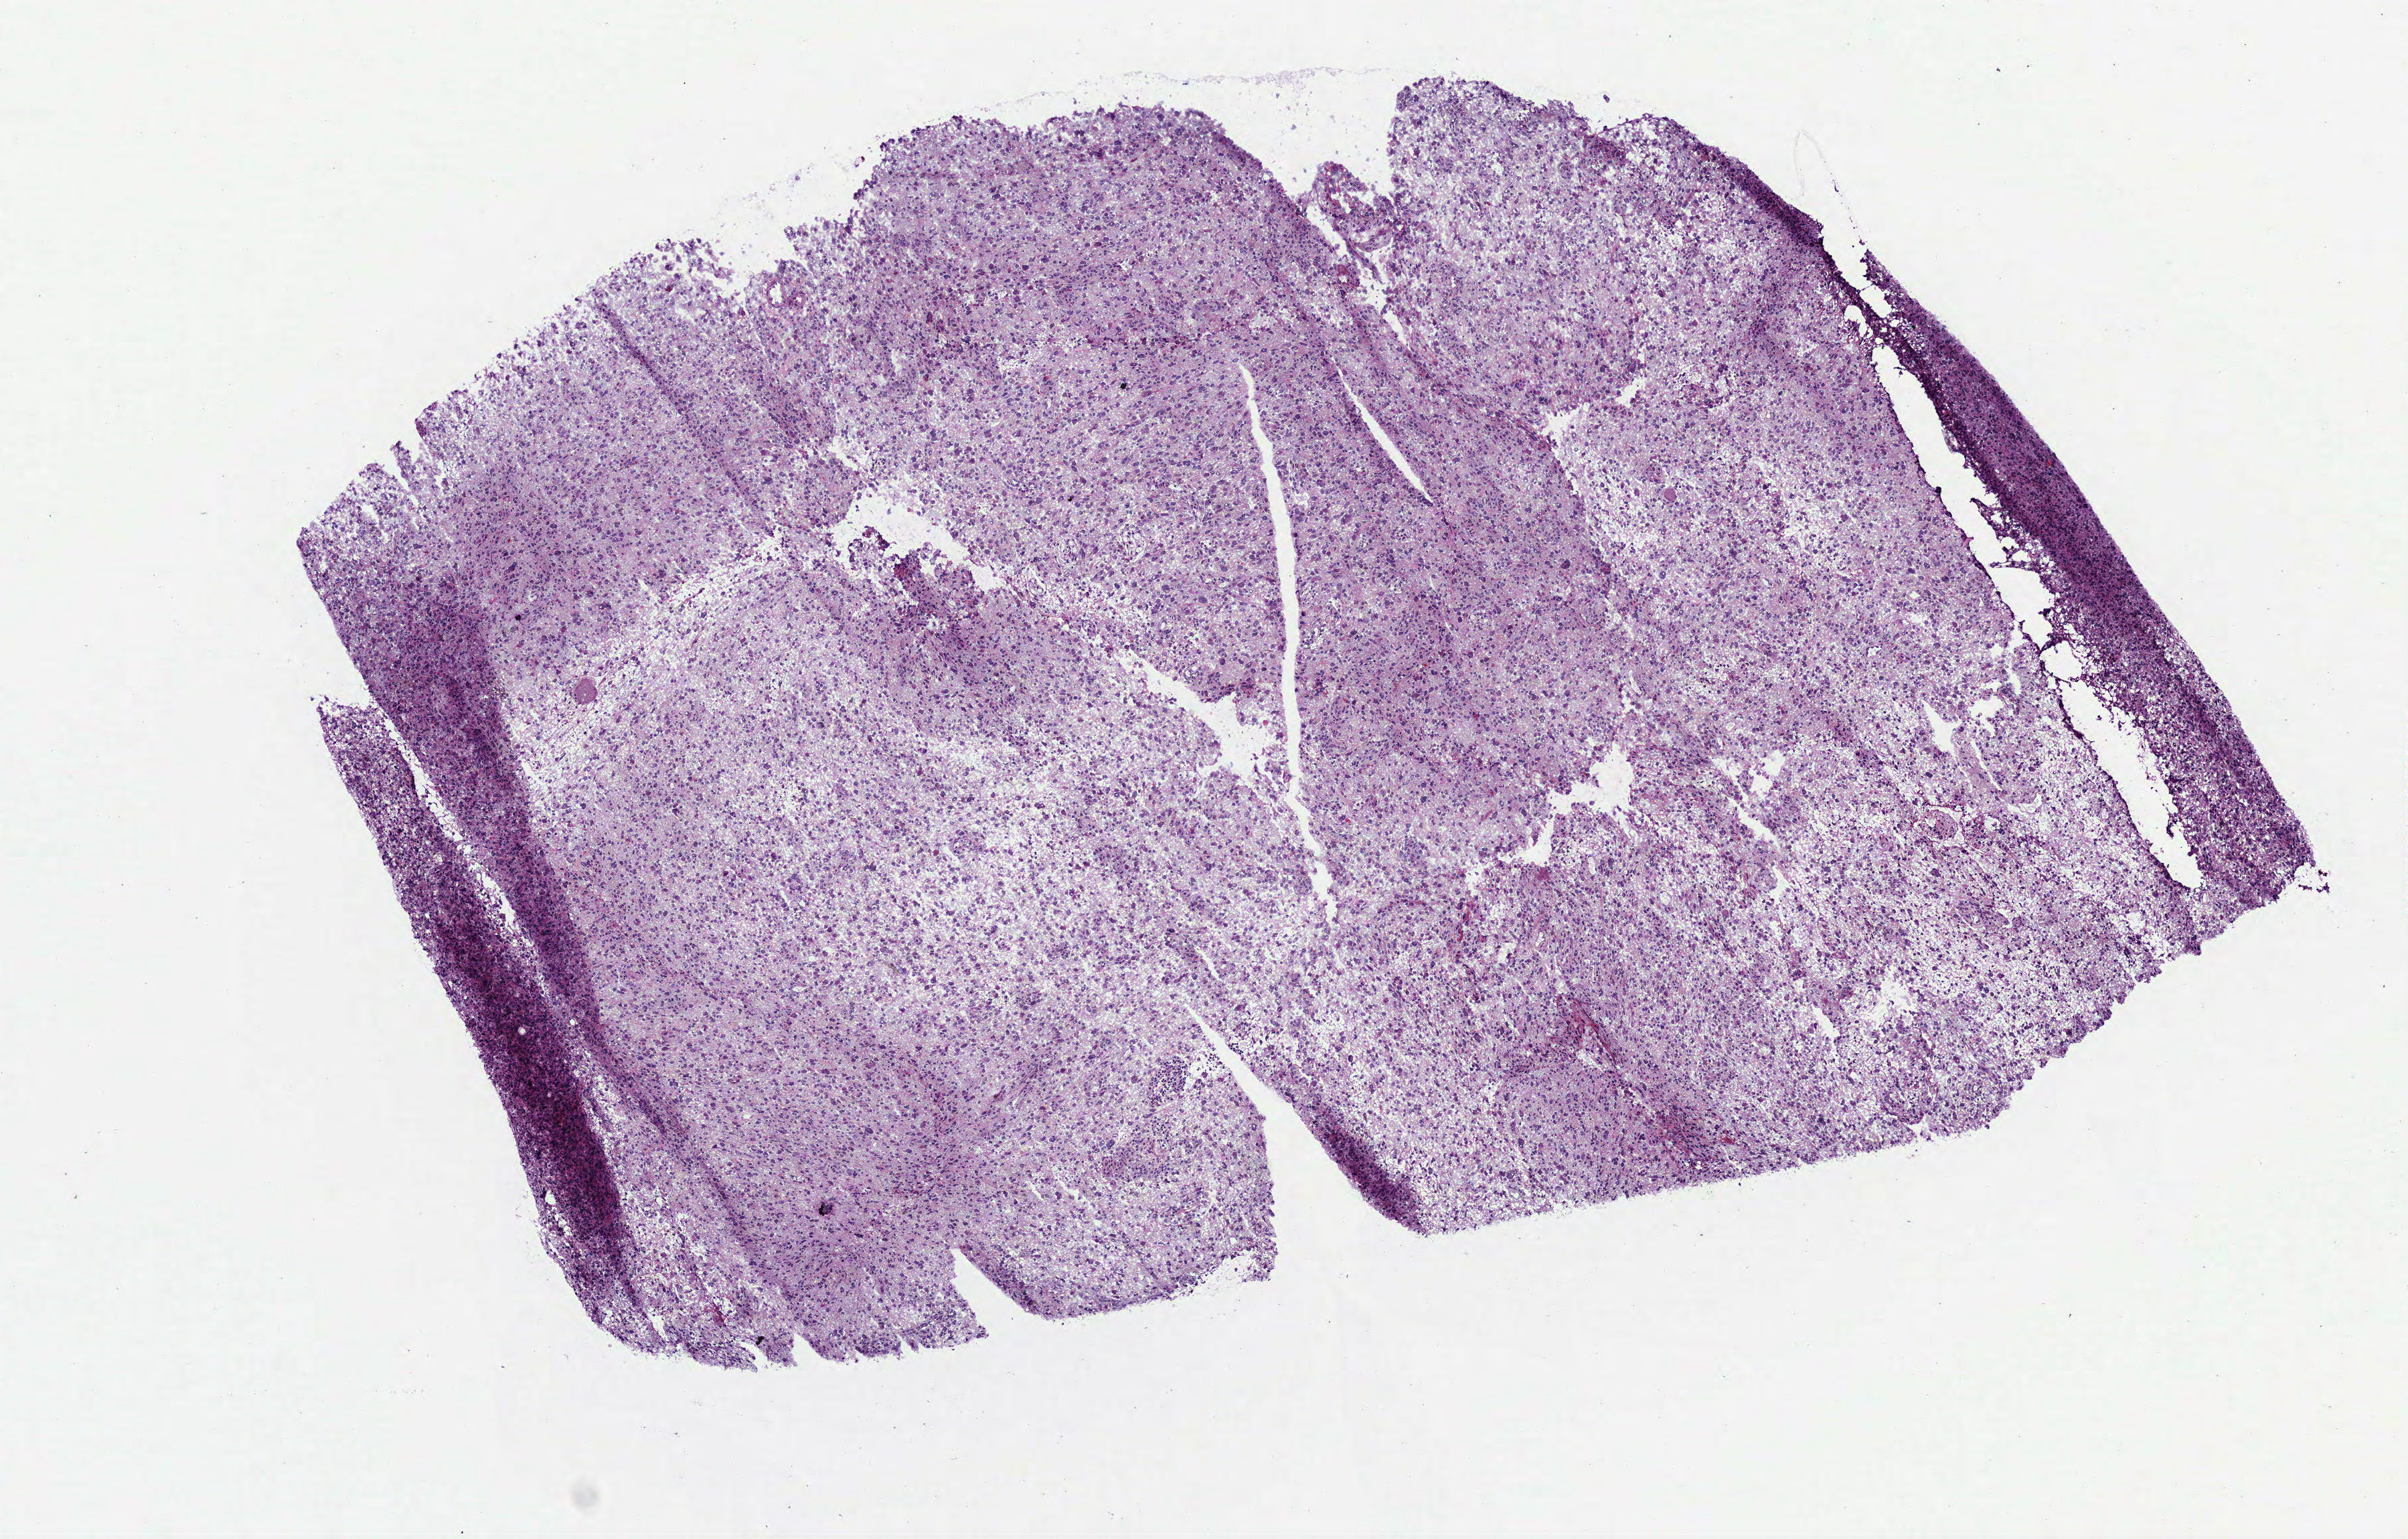
H&E whole-slide image, whole scanned area (about 7.3 x 4.6 mm, slide scanned at 40x) shown as a low-resolution overview. Frozen section. Sample: primary tumour, brain. Patient: female, age at initial diagnosis 24 years. Histologic grade: G3 (poorly differentiated). Slide review estimates, as recorded: tumour cells 100%, tumour nuclei 80%, normal cells 0%, stromal cells 0%, necrosis 0%.
Pathologic diagnosis: Astrocytoma, anaplastic (cerebrum).